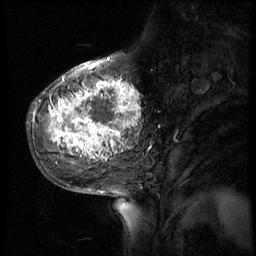
Breast MRI (dynamic contrast-enhanced), one sagittal slice; position 19 of 56 along the scan axis; 4 images stored at this slice position (order not interpretable as contrast timing); 1.5 T; TE 4.2 ms, TR 8.9 ms; 256 × 256 image matrix, field of view 220 × 220 mm. Female patient, age 51 years. From the clinical record (not read from this slice): setting: breast cancer imaged before/during neoadjuvant chemotherapy; receptor status: triple-negative.
Annotated regions visible in this slice (semi-automatic segmentation, software-assisted and operator-edited):
- analysis volume of interest (the breast-tissue region the enhancement analysis was run in; not a lesion): bounding box (x1, y1, x2, y2) in pixels: (30, 70, 150, 173)
- tumour enhancement mask (voxels above the 140 % enhancement threshold inside the analysis volume of interest): (35, 78, 140, 161)